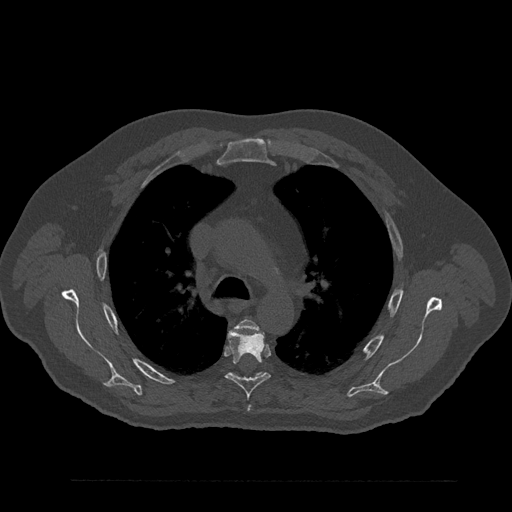
CT including the spine, one axial slice. Position 603 of 797 along the scan axis. 120 kVp. Bone window (W 1800 / L 400 HU). 512 × 512 image matrix, field of view 430 × 430 mm. Male patient, age 61 years. Case-level facts recorded for this patient, not image findings: primary cancer: prostate.
Annotated regions visible in this slice (semi-automatic segmentation, software-assisted and operator-edited):
- T4 vertebra: box from (x=237, y=319) to (x=258, y=411) px
- T5 vertebra: (x=226, y=330)–(x=271, y=399)
- T6 vertebra: (x=231, y=372)–(x=266, y=379)